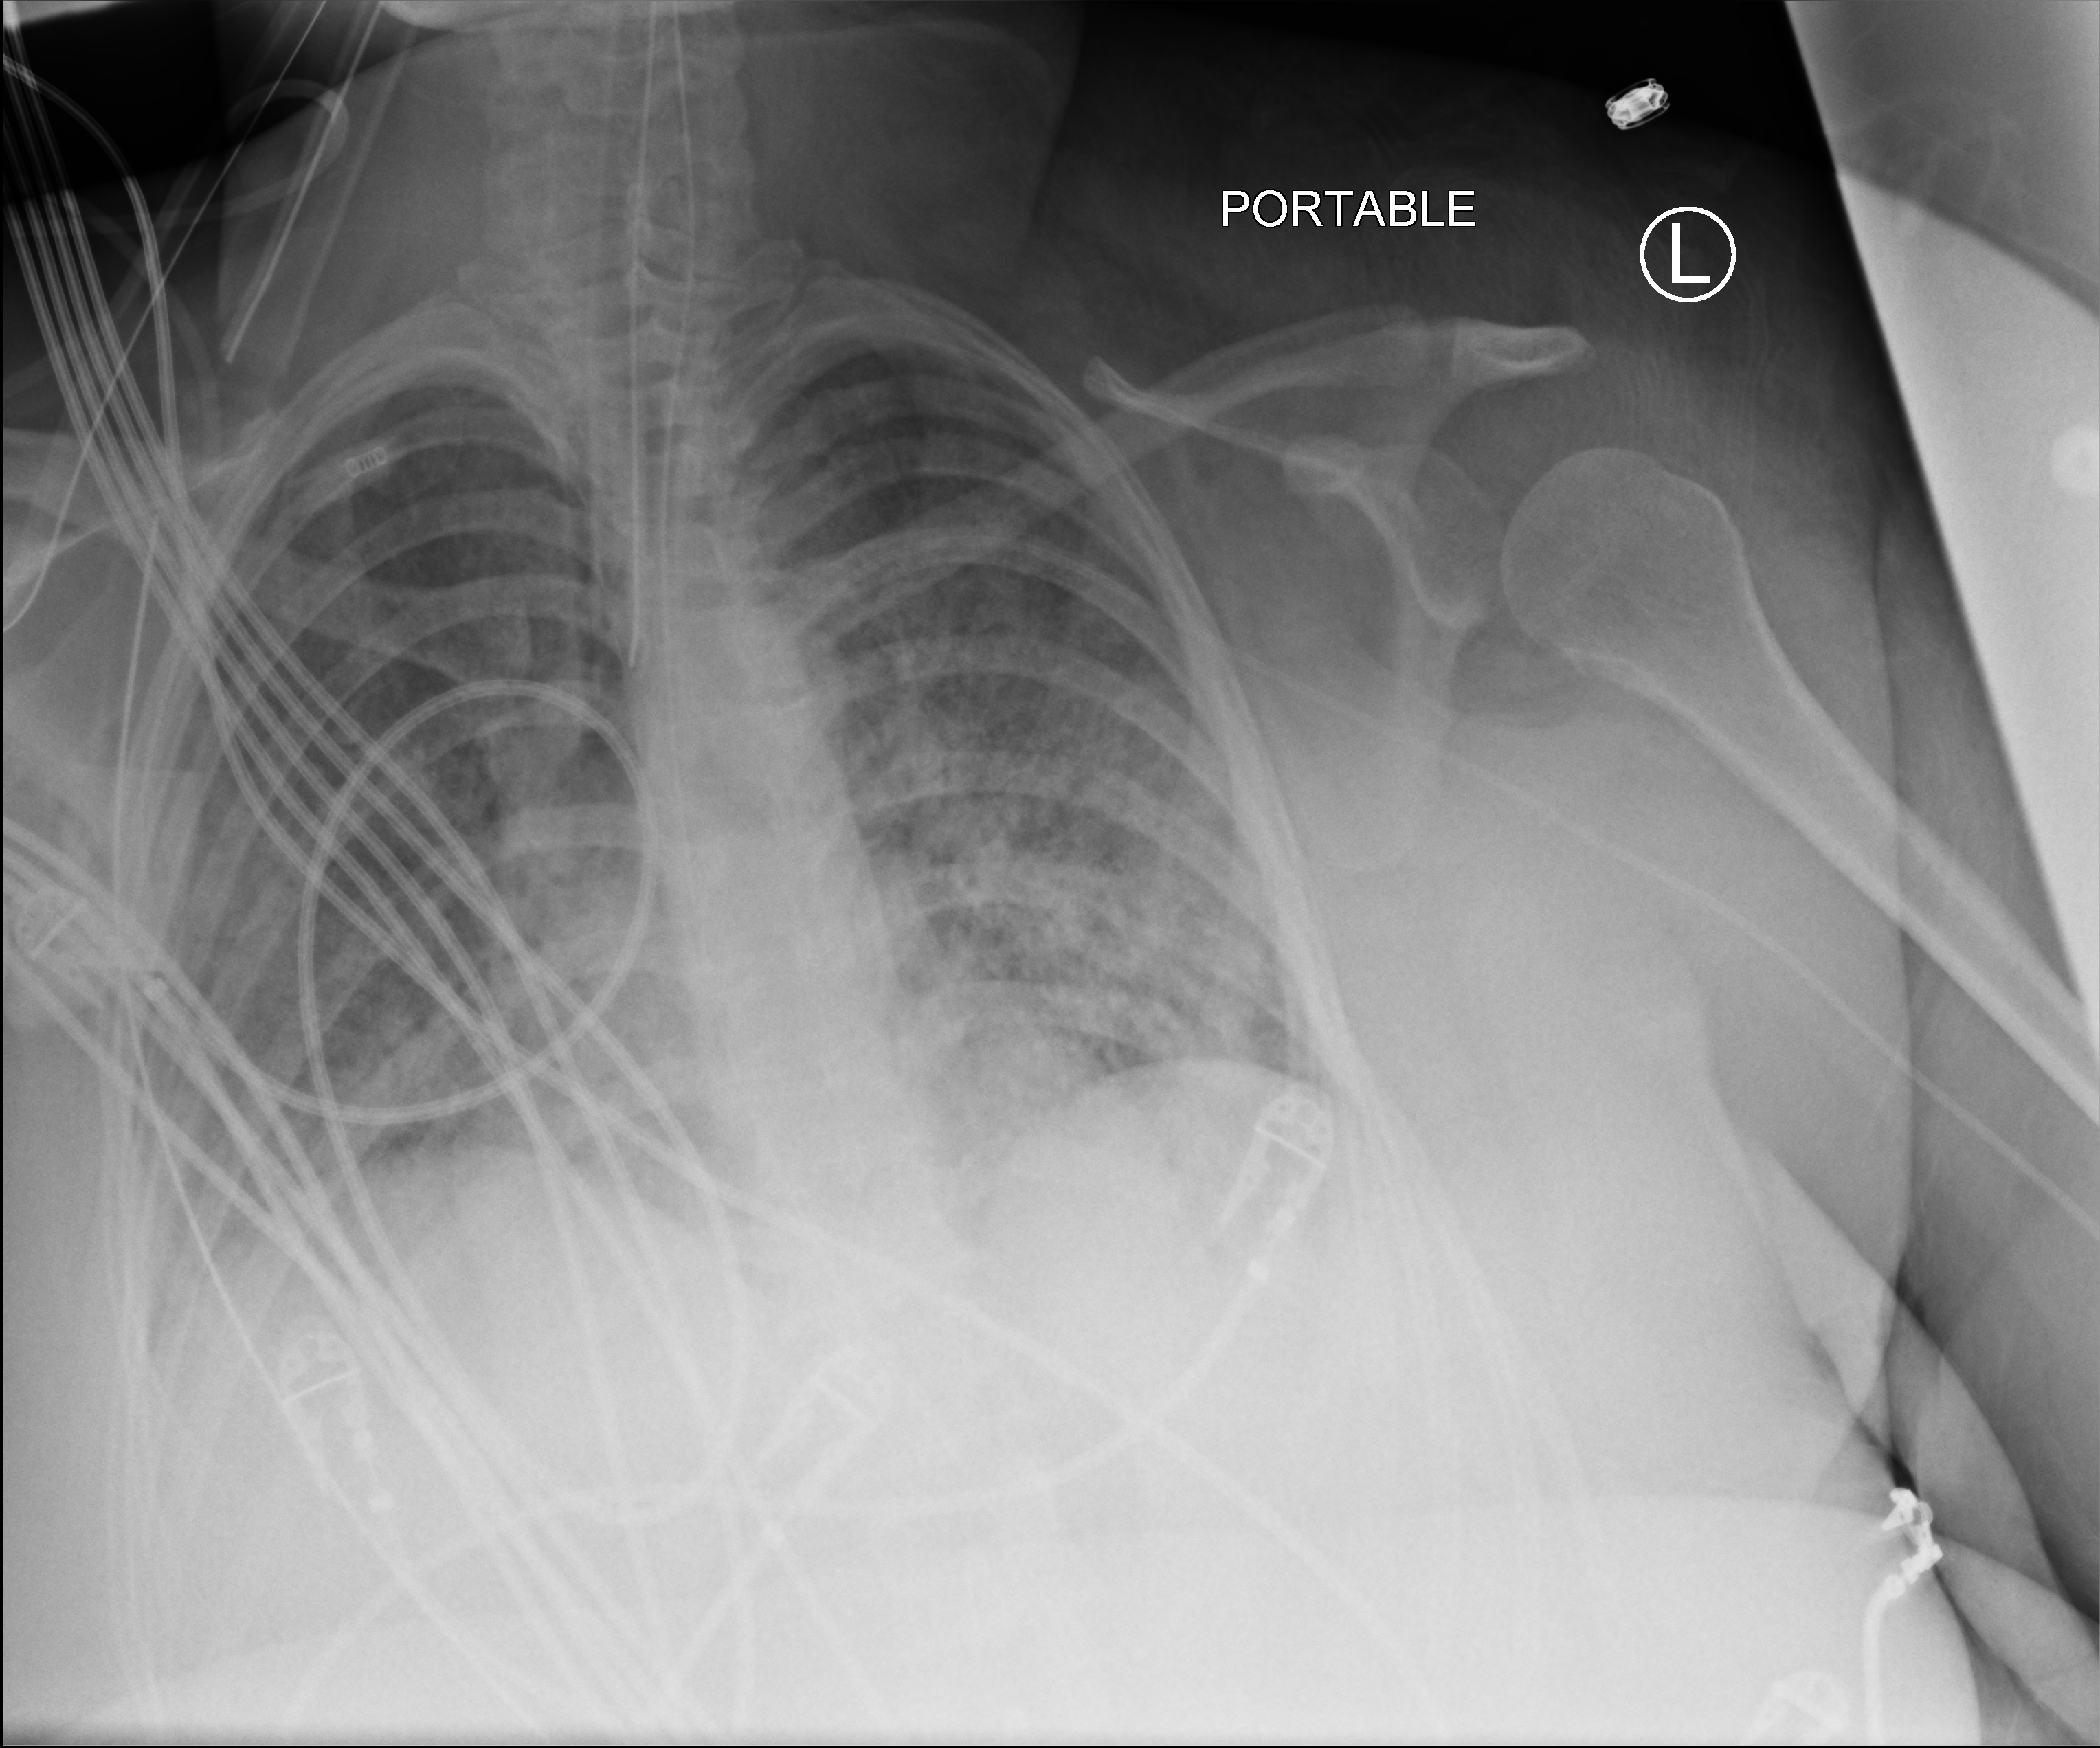
Chest X-ray (portable). Patient hospitalised with COVID-19; female, aged 18–59 years.
From the hospital-stay record, not from the radiograph (when in the stay this image was taken is not recorded): admitted to intensive care during this hospital stay: yes.